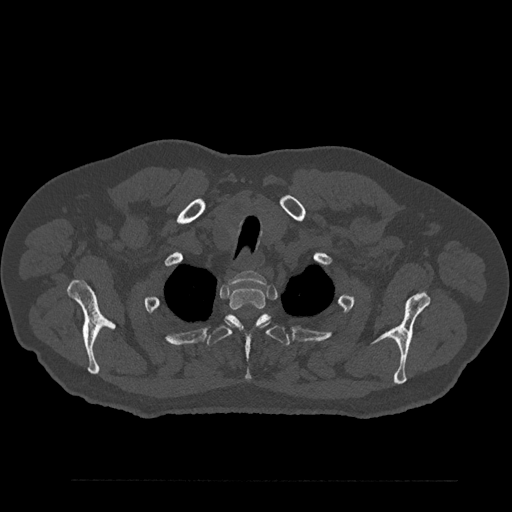
CT including the spine, one axial slice. Position 706 of 797 along the scan axis. Reconstruction kernel Br40s/3. 120 kVp. Bone window (W 1800 / L 400 HU). 512 × 512 image matrix. Patient: male, 61 years. Case-level facts recorded for this patient, not image findings: primary cancer: prostate.
Annotated regions visible in this slice (semi-automatically segmented with operator editing):
- T1 vertebra: bounding box (x1, y1, x2, y2) in pixels: (229, 271, 267, 285)
- T2 vertebra: (229, 287, 266, 327)
- T3 vertebra: (207, 314, 290, 381)